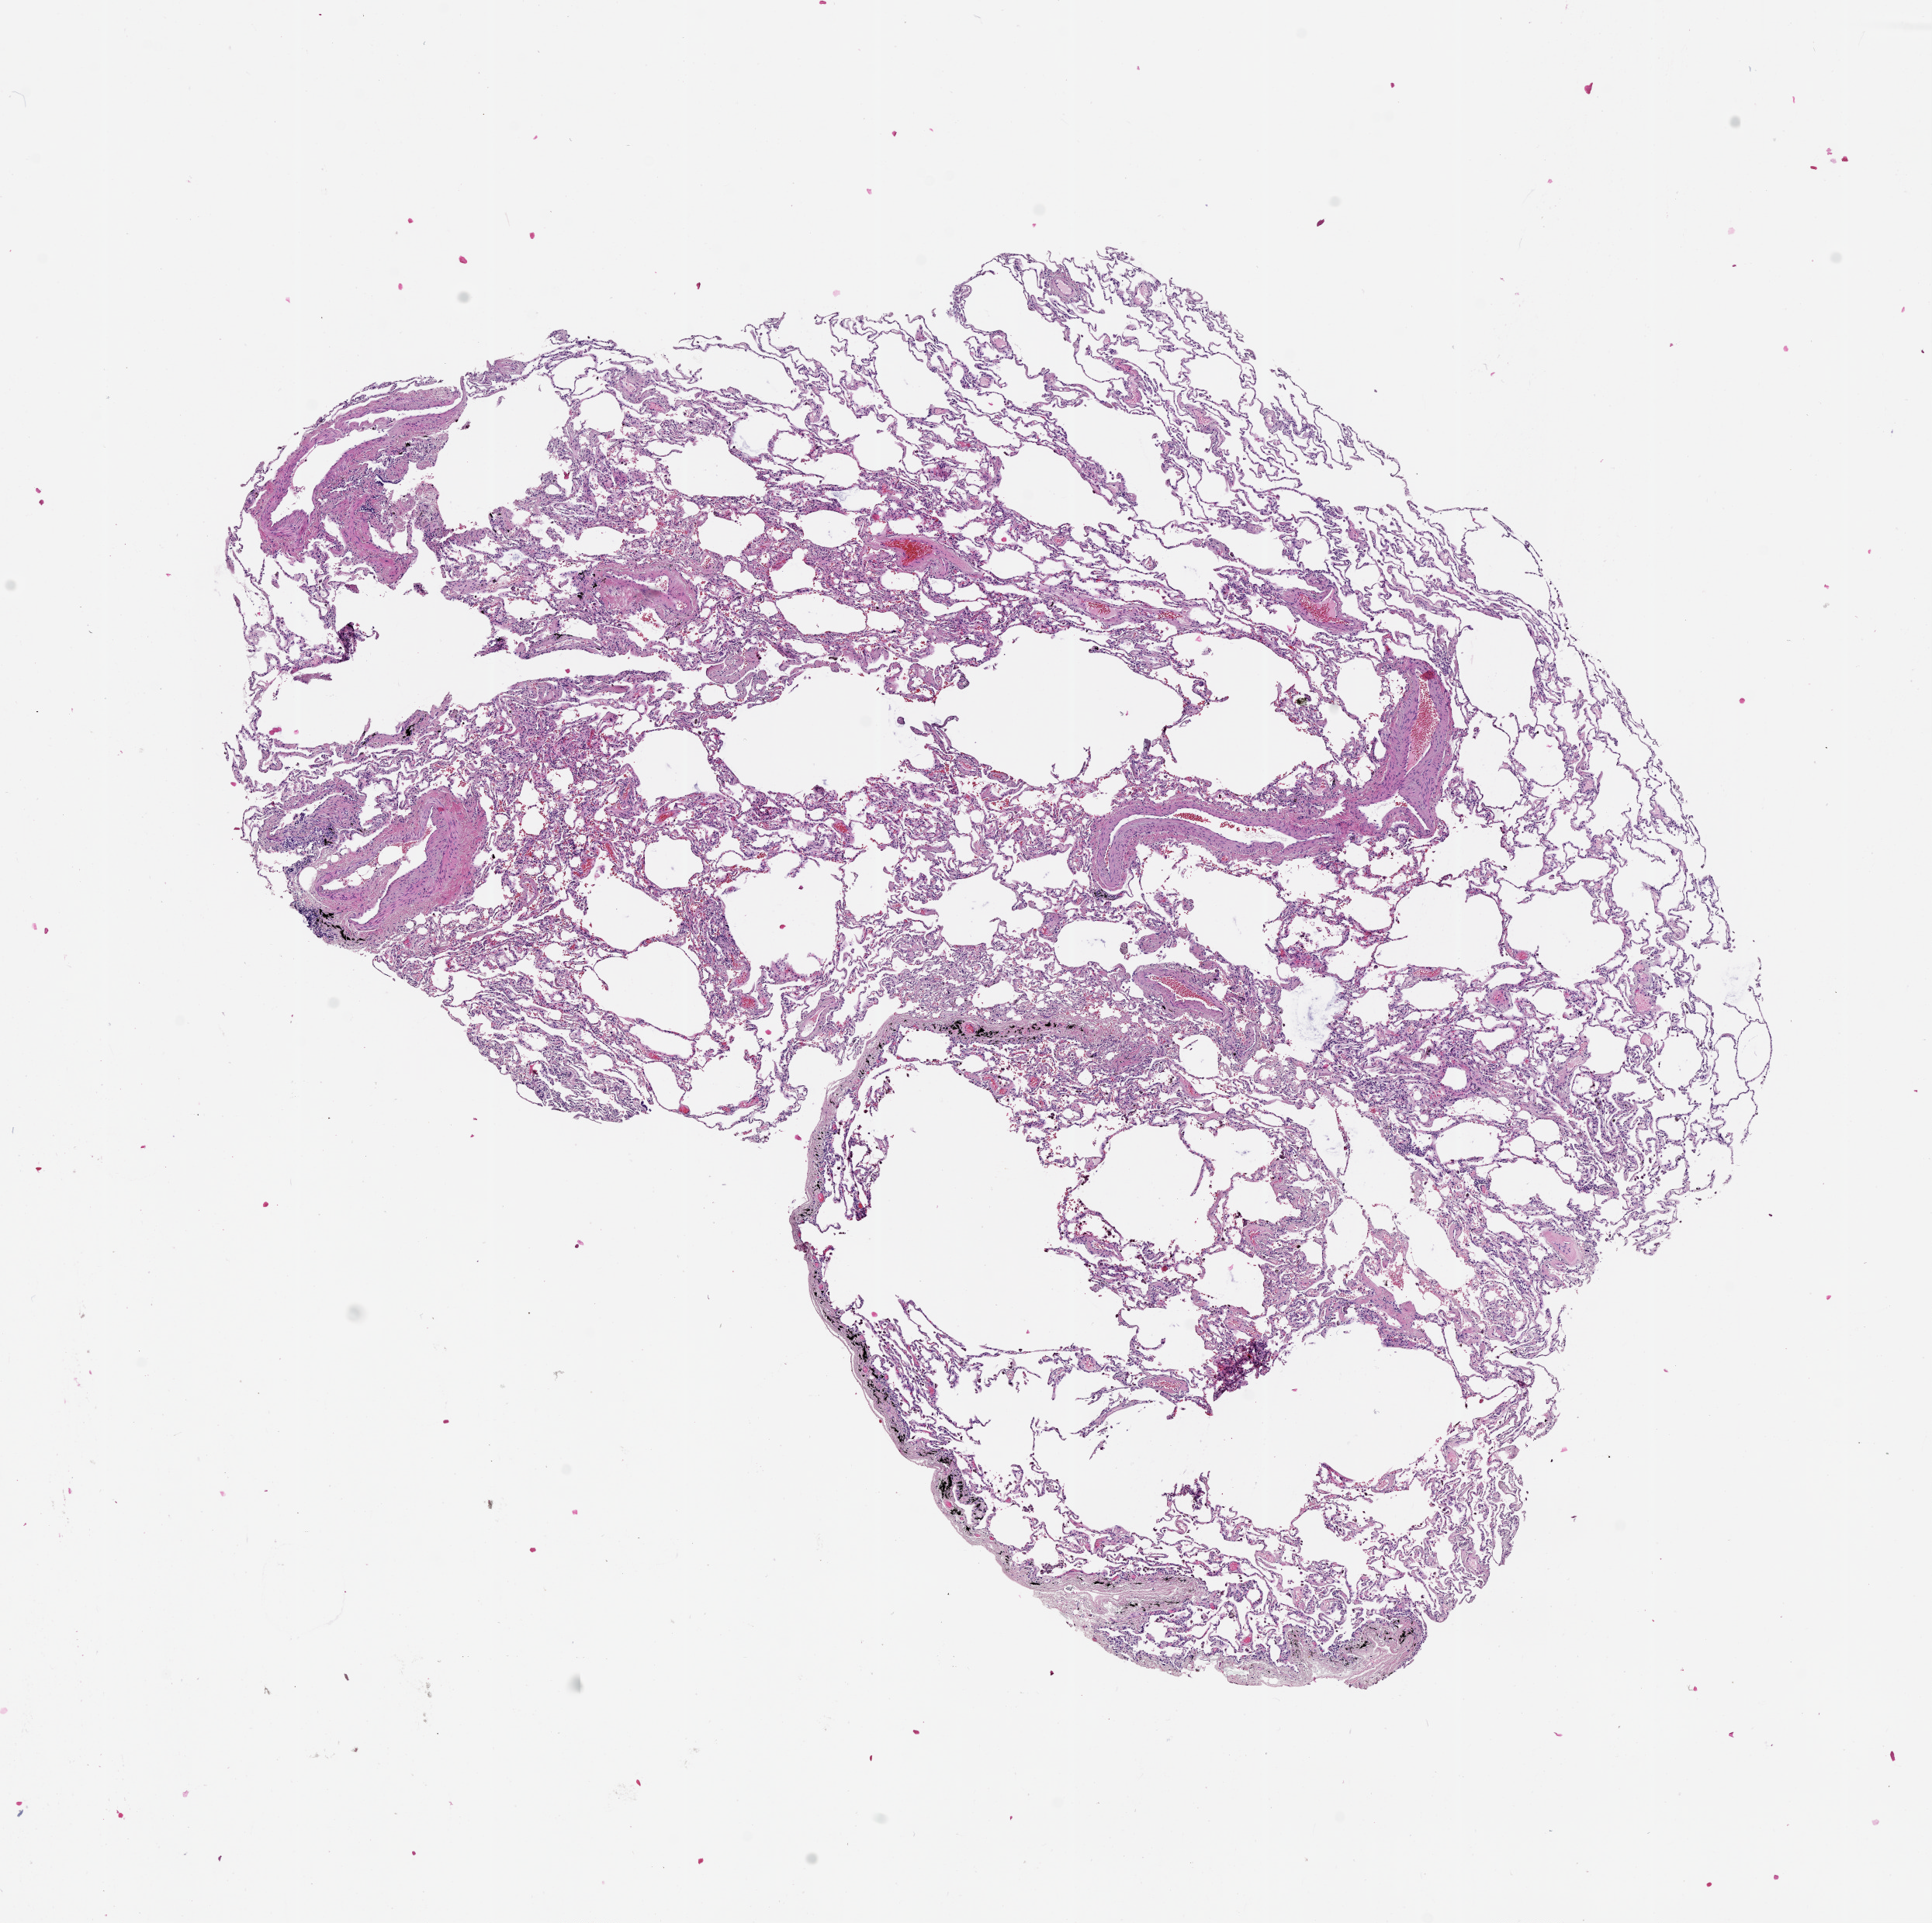
Digitized H&E-stained tissue section (whole slide), low-resolution overview of the scanned area, about 10.0 x 10.0 mm (from a 20x scan), lung, normal (non-tumour) tissue. Male, 67 y/o.
This section: normal (non-tumour) tissue from the same patient. Patient diagnosis (cohort enrolment): squamous cell carcinoma (lung).